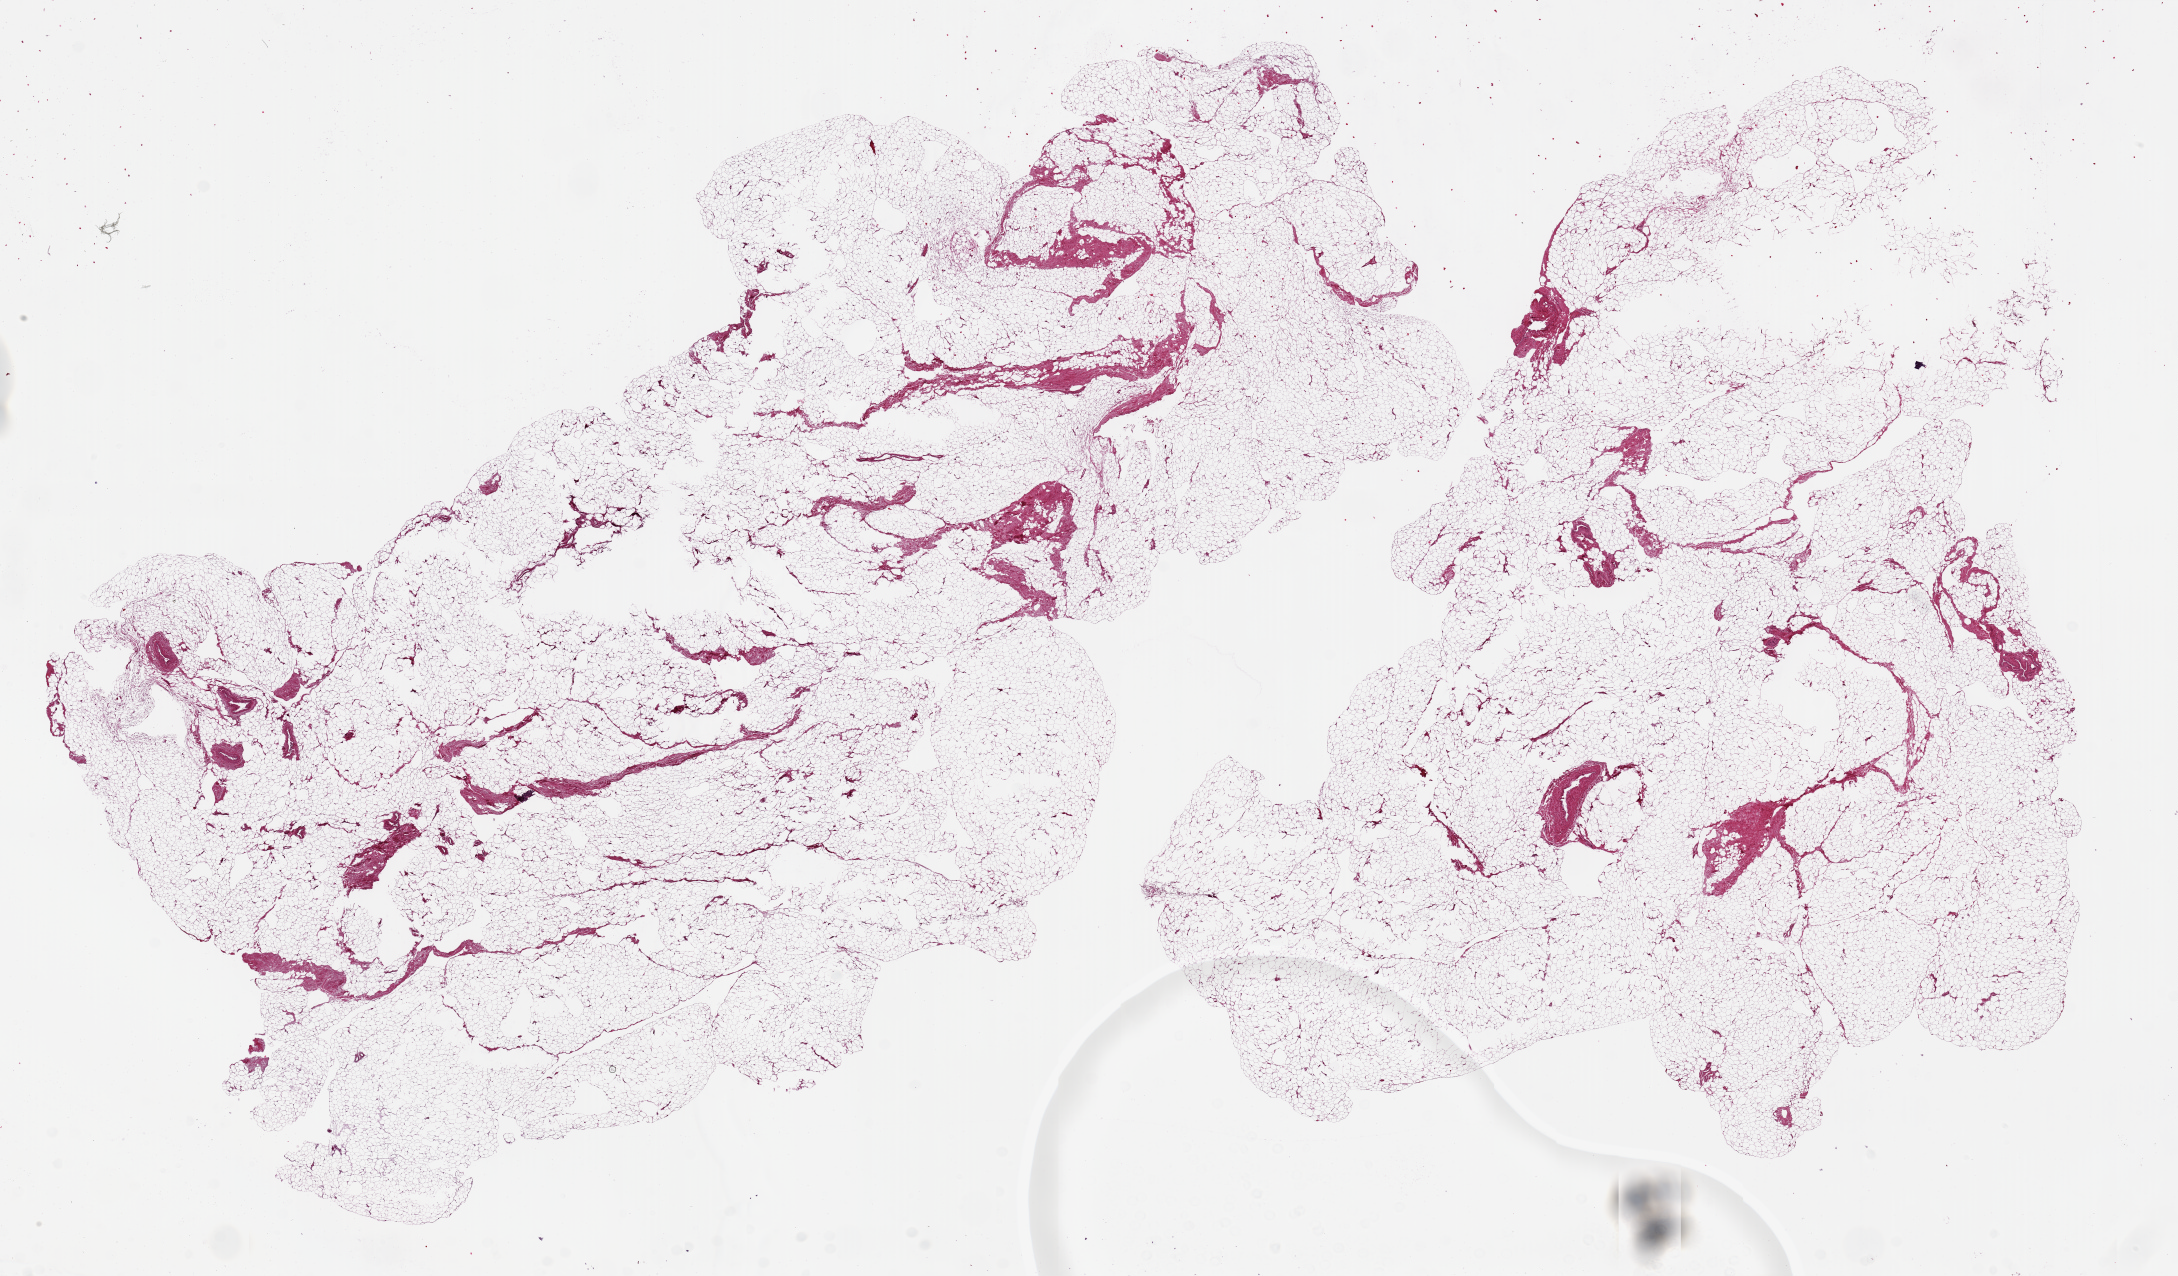
Whole-slide image, hematoxylin and eosin (H&E) stain, brightfield — shown as a low-resolution overview of the whole scanned area (about 34.5 x 20.2 mm, acquisition: 20x scan), PAXgene-fixed paraffin-embedded (PFPE) section, target tissue: adipose tissue, tissue donor sample.
Pathologist's review note for this sample: 2 aliquots, ~15x10mm.